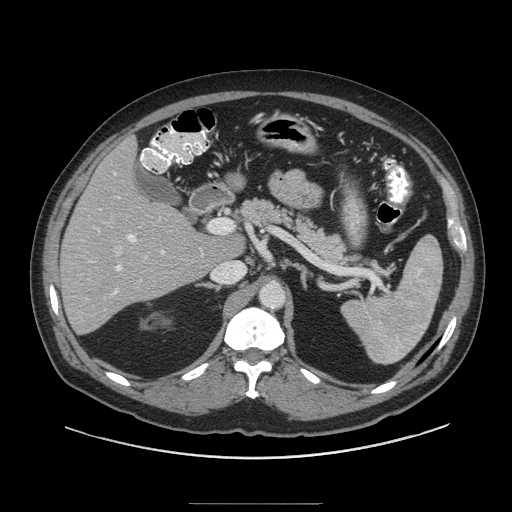
Contrast-enhanced abdominal CT (liver protocol), one axial slice. Soft-tissue window (W 400 / L 40 HU). 2.5 mm slice thickness. 512 × 512 image matrix, field of view 440 × 440 mm. Case-level facts recorded for this patient, not image findings: diagnosis: hepatocellular carcinoma (patient treated with transarterial chemoembolisation; whether this scan precedes or follows treatment is not stated here); TNM stage (as recorded): Stage-I; Child-Pugh class: A; tumour size: 4 cm.
Structures marked on this image (semi-automatic segmentation, software-assisted and operator-edited):
- liver parenchyma outside the tumour (the mass and vessels are separate outlines, so this box may not span the whole liver): bounding box <58,136,233,334> (left, top, right, bottom; pixels)
- liver vessels: <113,173,165,294>